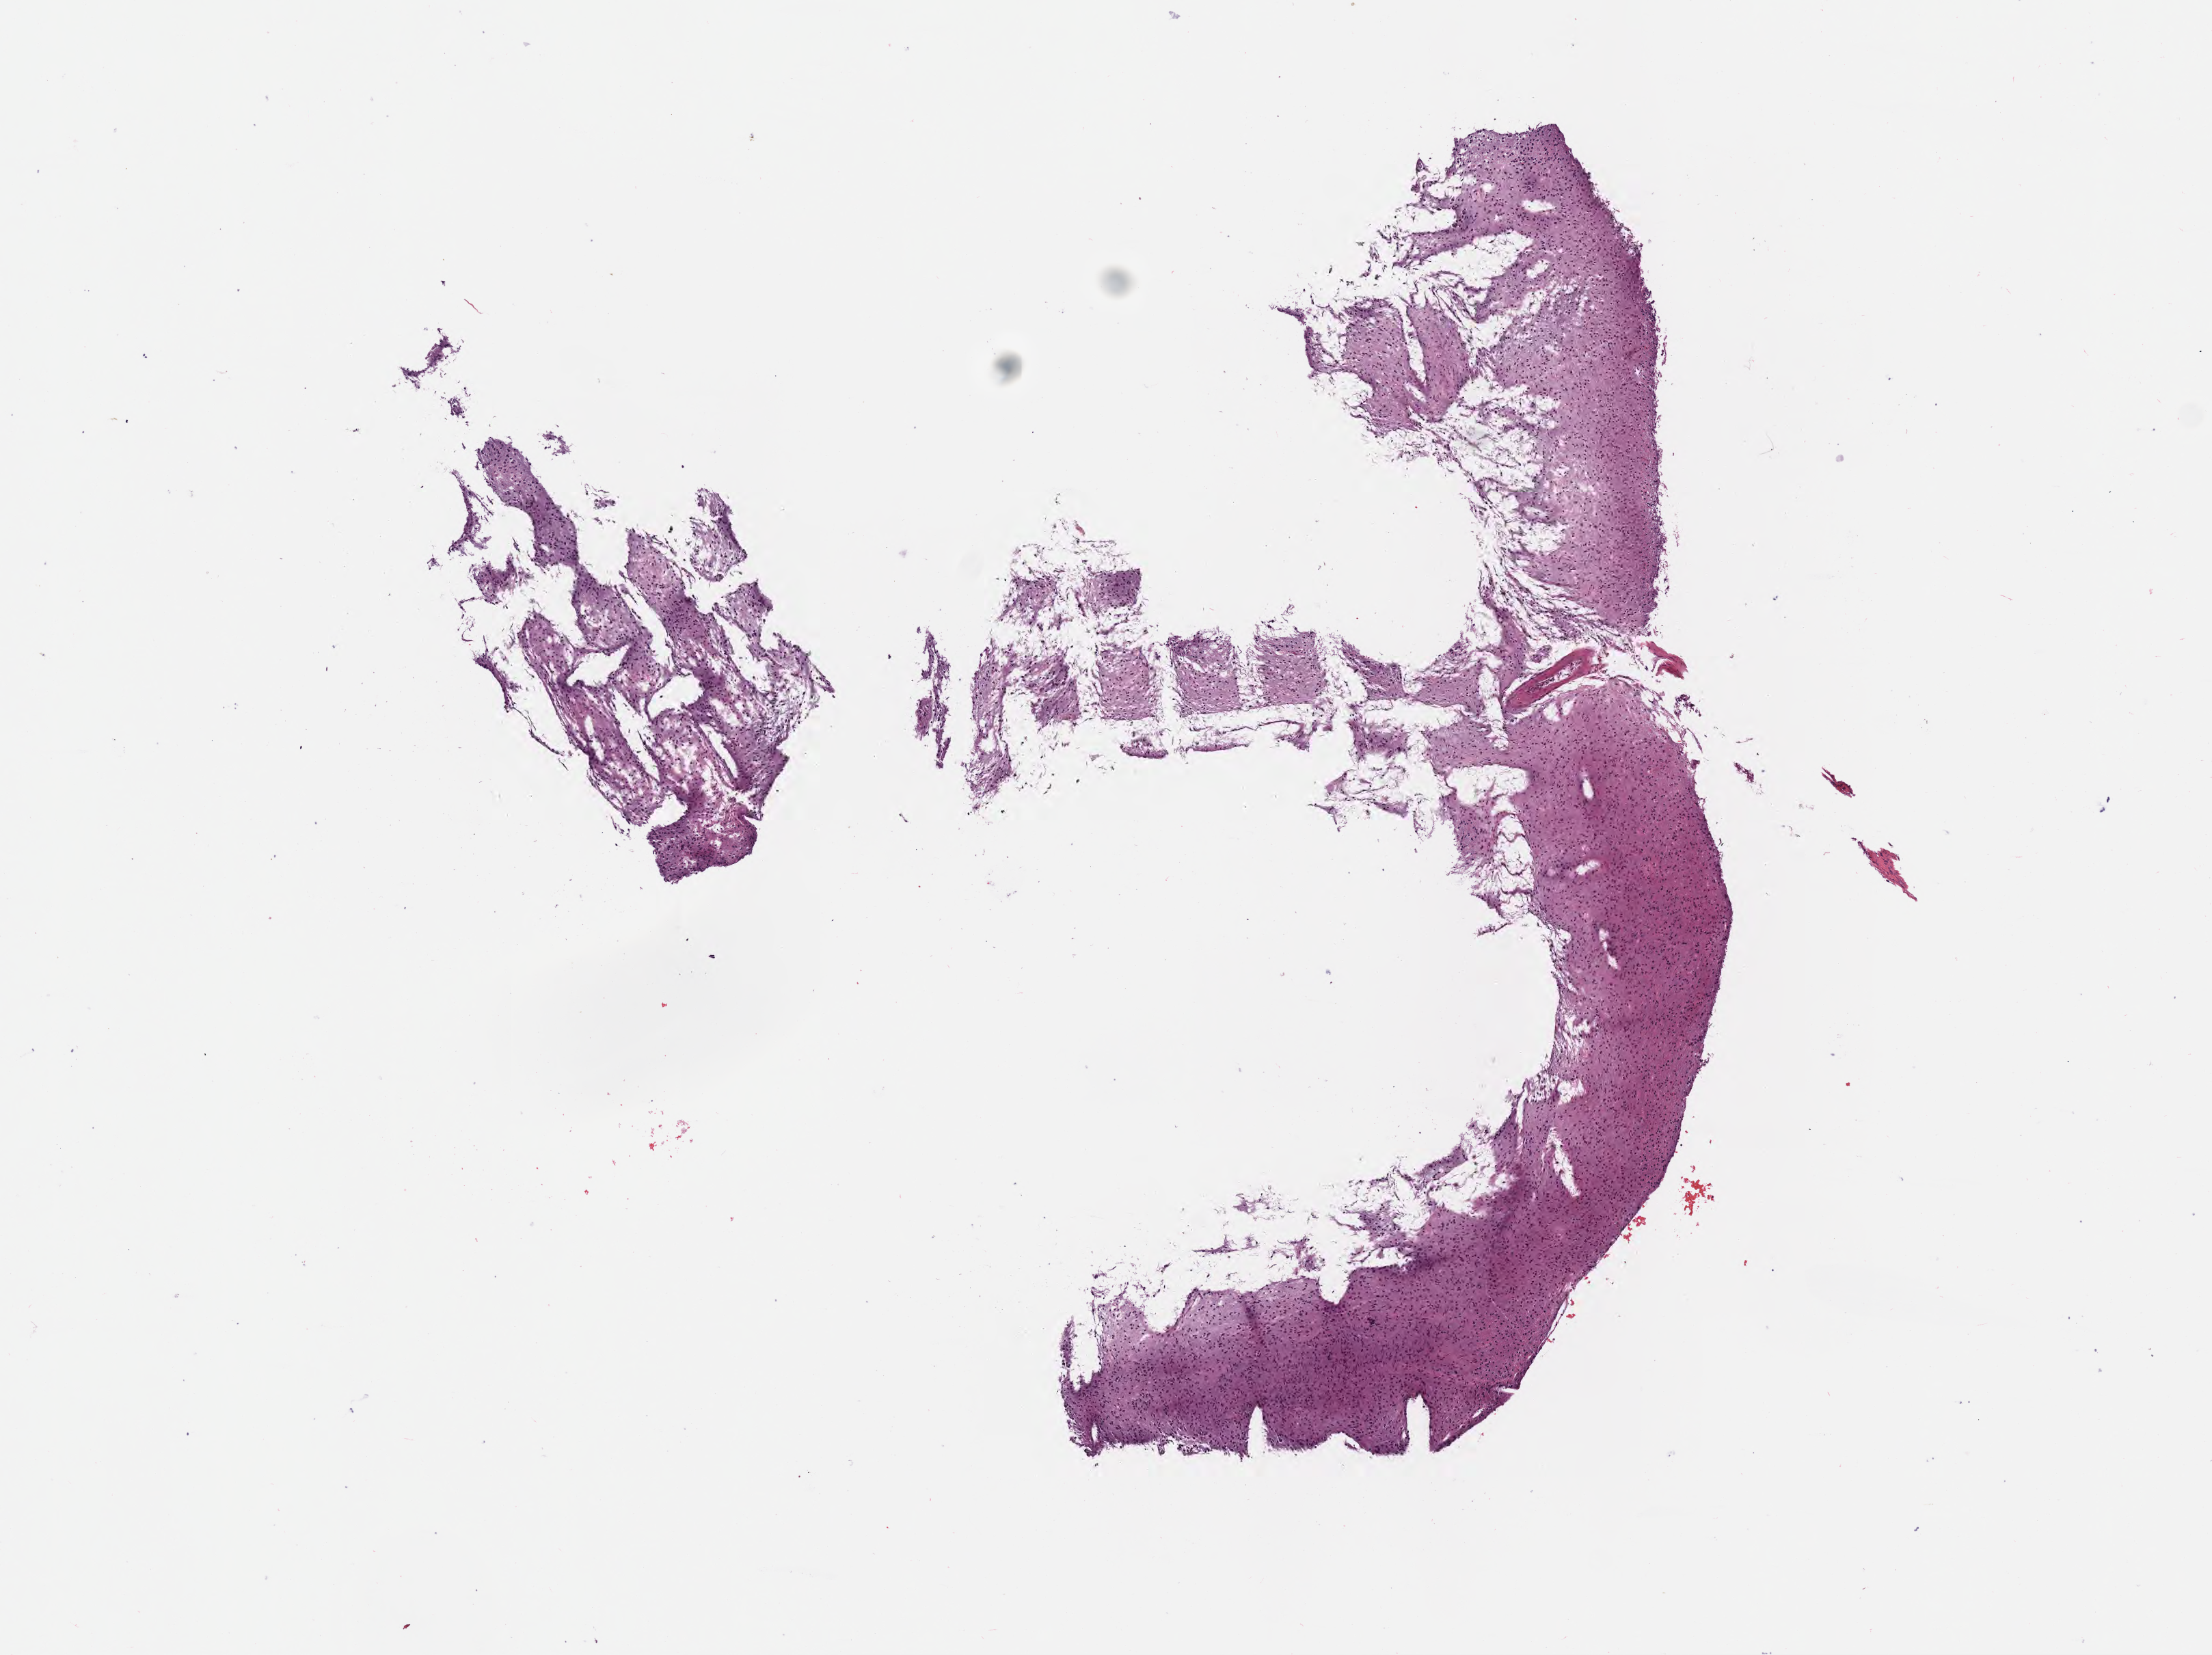
Digitized Hematoxylin and eosin (H&E) stained tissue section (whole slide) — shown as a low-resolution overview of the whole scanned area (about 6.5 x 4.9 mm, slide scanned at 40x), formalin-fixed paraffin-embedded (FFPE) diagnostic section, primary tumour sample from the brain. Patient: male, age at initial diagnosis 38 years. Histologic grade: G2 (moderately differentiated).
Histologic diagnosis: Oligodendroglioma, NOS (cerebrum).